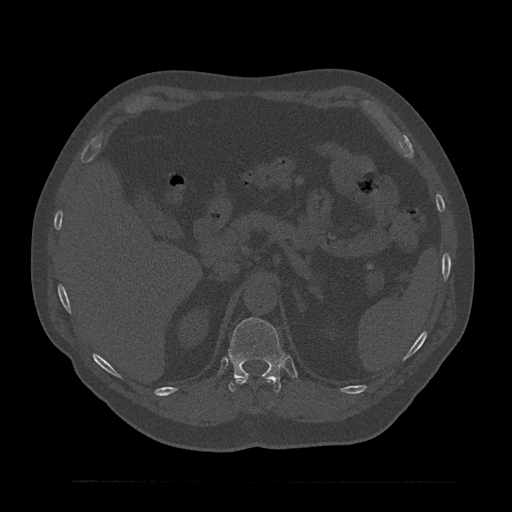
CT including the spine, one axial slice; slice 251 of 797 in the series (ordered by position); reconstruction kernel Br40s/3; 120 kVp; bone window (W 1800 / L 400 HU); 0.5 mm slice thickness; 512 × 512 image matrix. Patient: male, 61 years. From the clinical record (not read from this slice): primary cancer: prostate.
Outlined on this slice (semi-automatic segmentation, software-assisted and operator-edited):
- T11 vertebra: bounding box (x1, y1, x2, y2) in pixels: (236, 378, 273, 385)
- T12 vertebra: (228, 317, 285, 393)